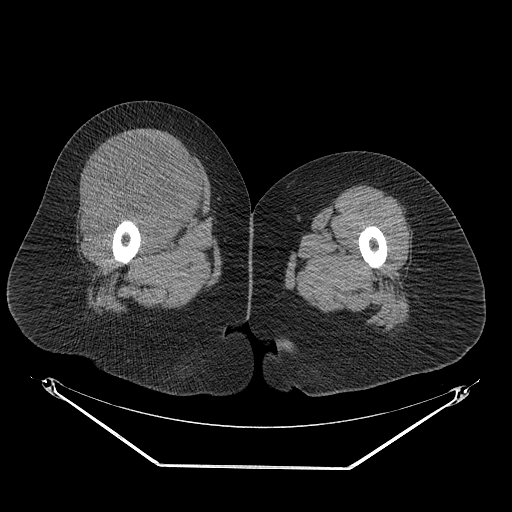
CT of an extremity soft-tissue mass (from a PET/CT study), one axial slice; slice 38 of 267 in the series (ordered by position); 140 kVp; soft-tissue window (W 400 / L 40 HU); 3.75 mm slice thickness; 512 × 512 image matrix. Female patient. From the clinical record (not read from this slice): histological type: malignant solitary fibrous tumor; grade: intermediate; site of the primary tumour: right thigh.
Outlined on this slice (expert contour drawn on MRI and transferred to this co-registered scan by the dataset authors):
- gross tumour volume including surrounding oedema: box from (x=82, y=135) to (x=209, y=231) px
- gross tumour volume (mass): (x=89, y=135)–(x=204, y=227)